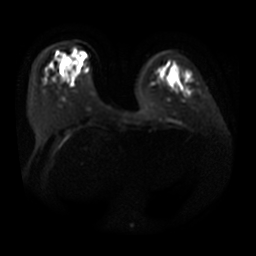
Breast MRI, one axial slice. Position 10 of 31 along the scan axis. Diffusion-weighted series; image 2 of 4 stored at this slice position (different b-values; order by instance number). 3 T. 5 mm slice thickness. 256 × 256 image matrix. Female patient.
Structures marked on this image (expert manual segmentation):
- tumour on diffusion-weighted imaging: bounding box [x1, y1, x2, y2] px = [62, 59, 71, 67]